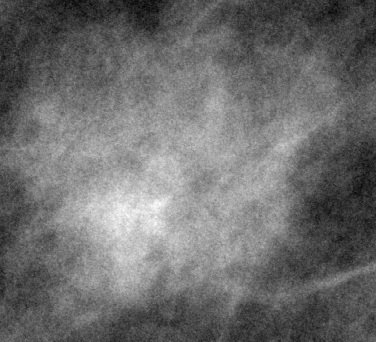
Cropped region of a digitized screen-film mammogram centred on a radiologist-marked abnormality, right breast, MLO view, BI-RADS breast density category 2 (scale 1–4).
- Marked abnormality: mass, shape oval, margins microlobulated; BI-RADS assessment category 4; subtlety rating 3 on a 1 (subtle) to 5 (obvious) scale; pathology result (as recorded, not read from the image): benign.